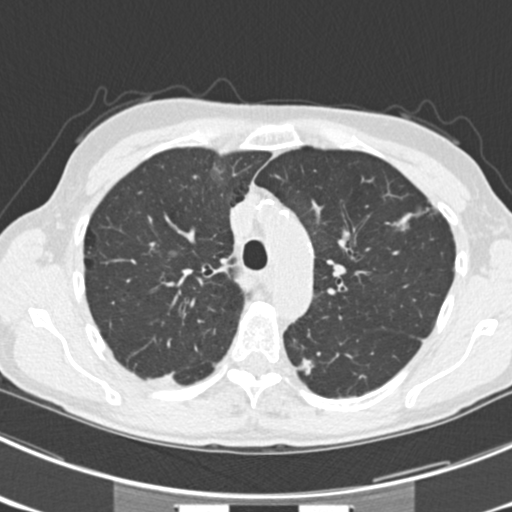
Low-dose screening chest CT, one axial slice; slice 164 of 225 in the series (ordered by position); reconstruction kernel B30f; 120 kVp; lung window (W 1500 / L -600 HU); 2 mm slice thickness; 512 × 512 image matrix, field of view 302 × 302 mm.
Structures marked on this image (outlined manually by an expert reader):
- lesion 2 (tumor, lower lobe of left lung): bounding box <298,357,316,376> (left, top, right, bottom; pixels)